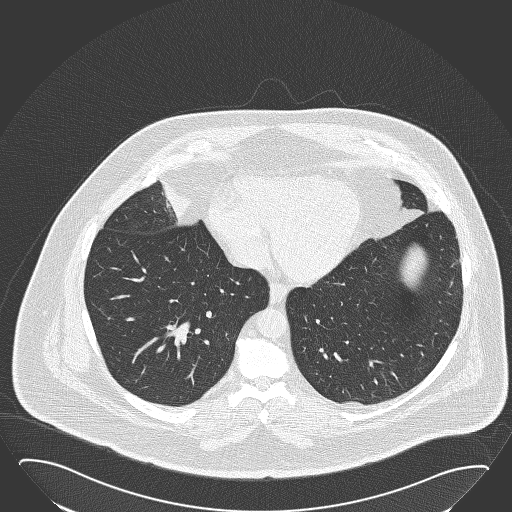
Low-dose screening chest CT, one axial slice. Lung window (W 1500 / L -600 HU). 2 mm slice thickness. 512 × 512 image matrix.
Annotated regions visible in this slice (outlined manually by an expert reader):
- lesion 1 (tumor, hilum of right lung): box from (x=161, y=182) to (x=189, y=222) px